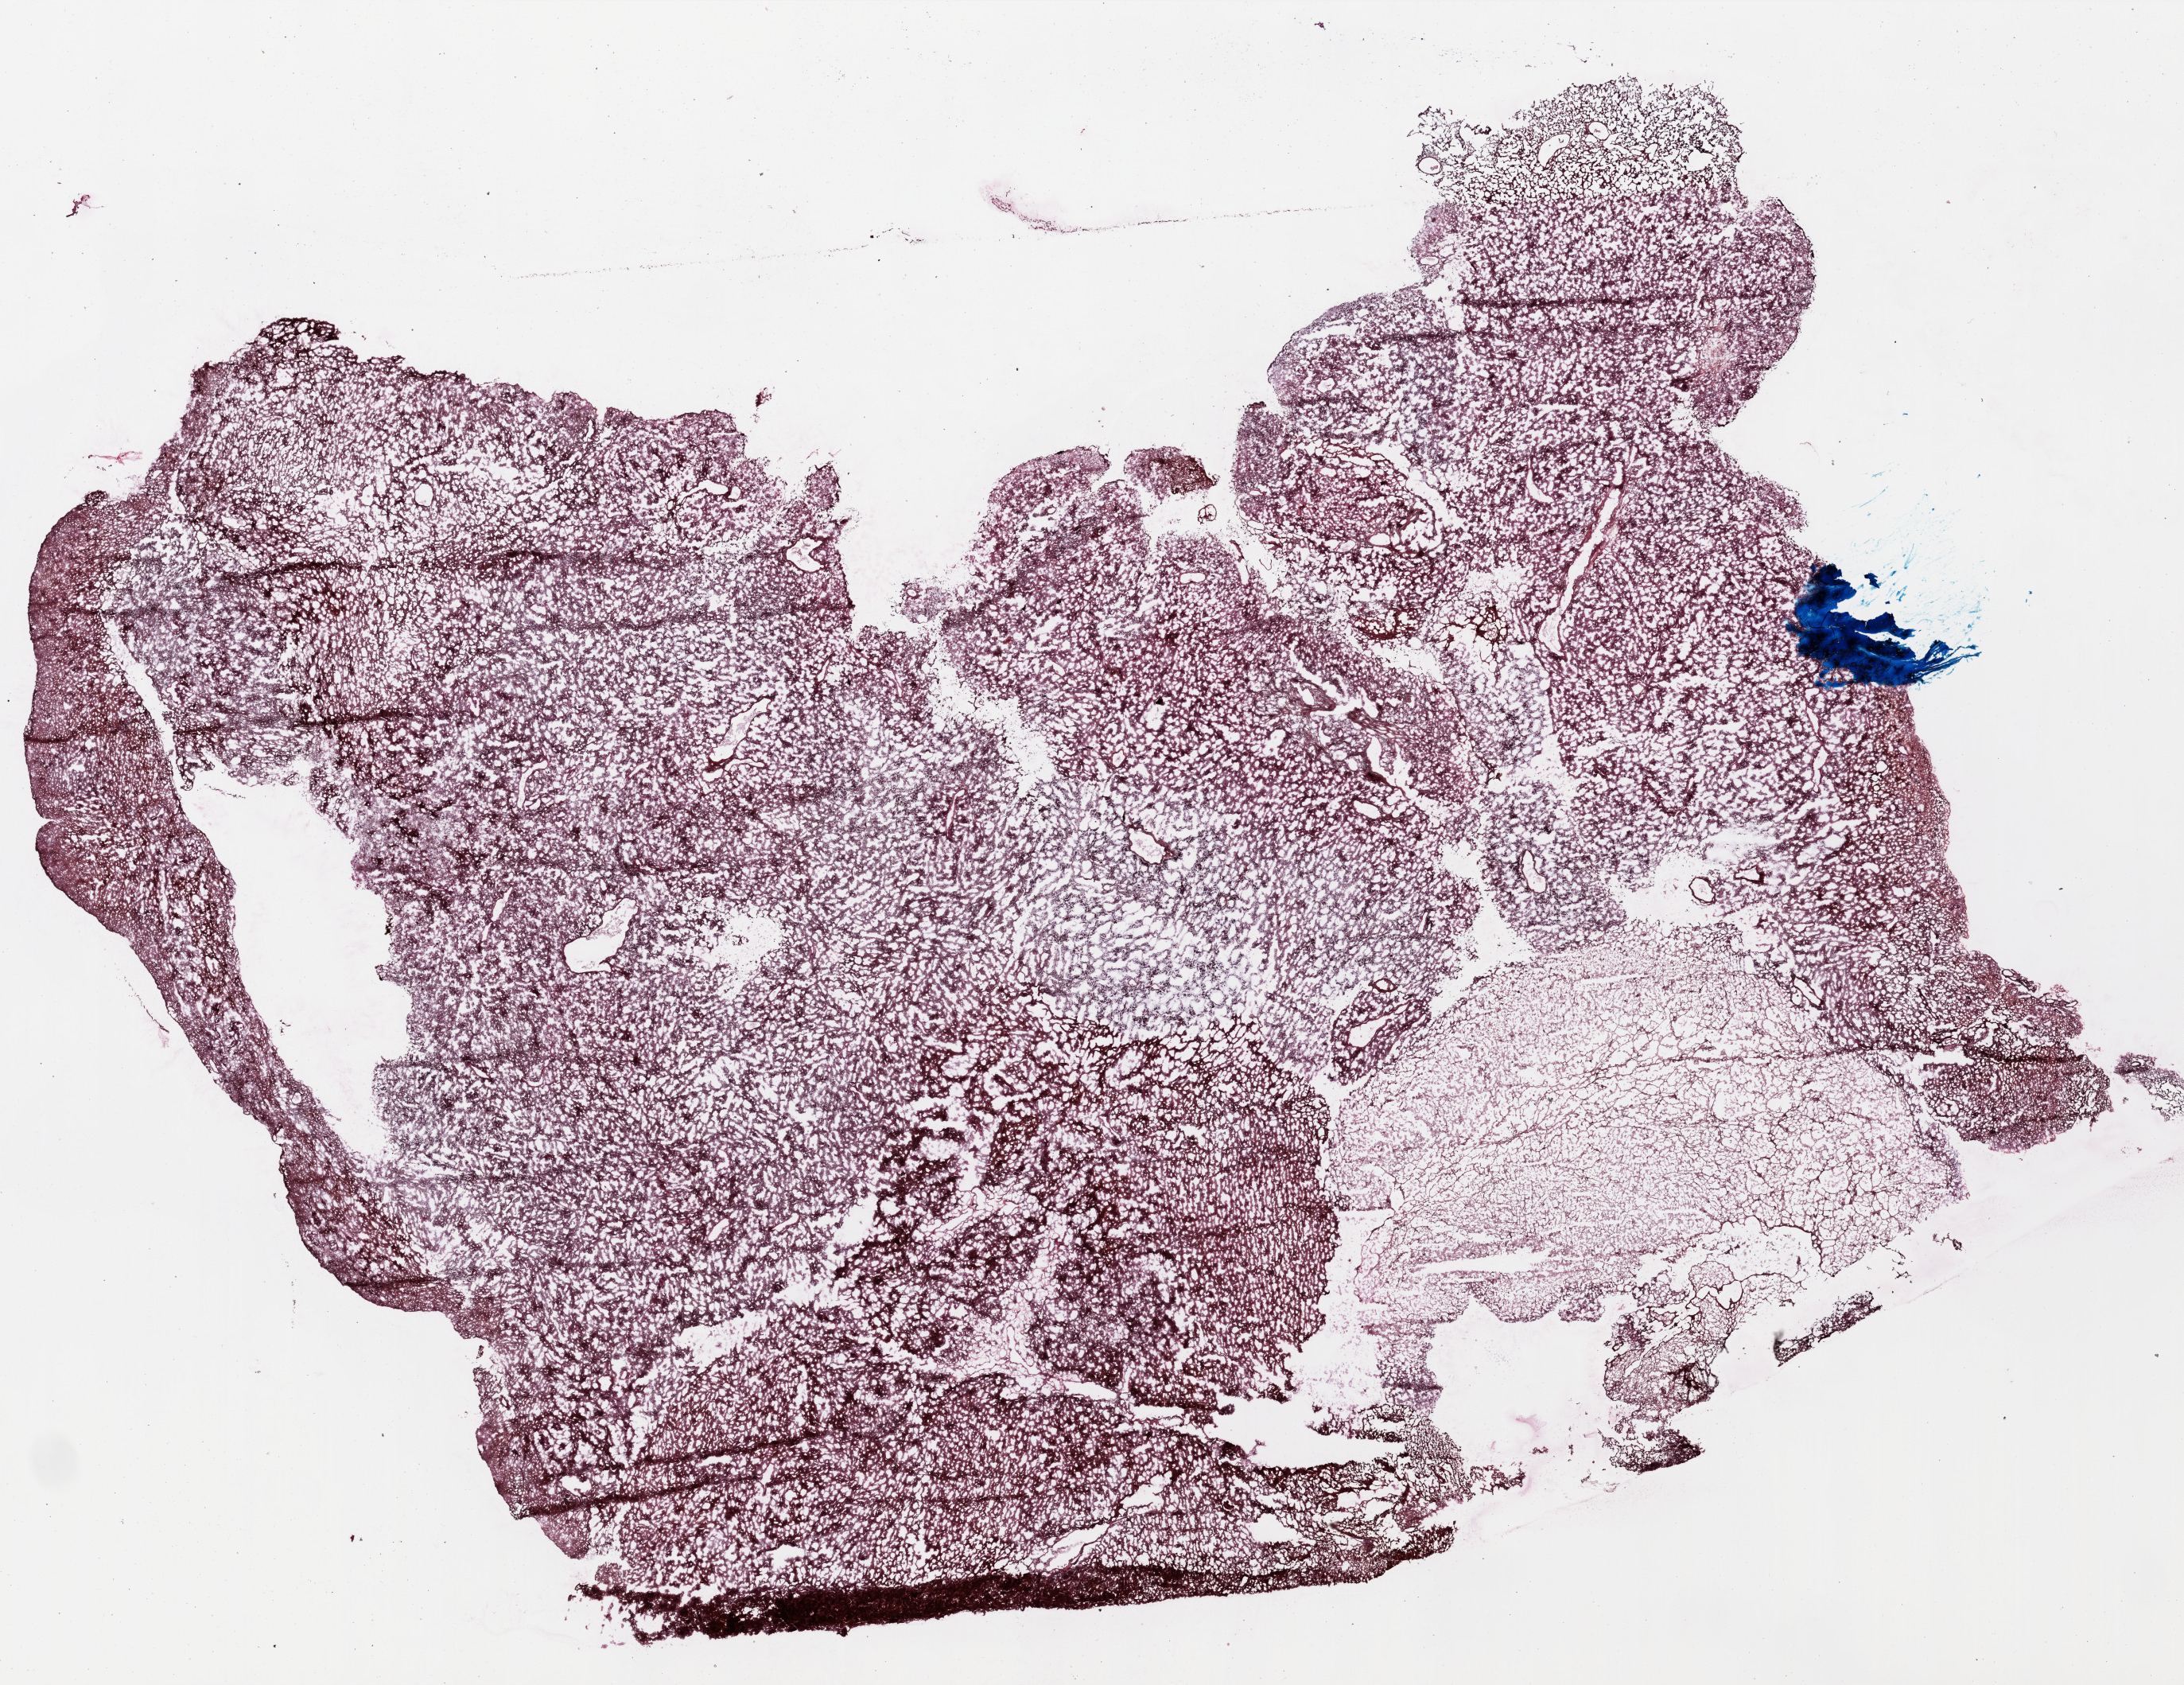
H&E-stained whole-slide image, a low-resolution overview of the entire scanned area, about 22.0 x 17.0 mm. Frozen section. Primary tumour sample from the brain. Male, age 48 years at initial diagnosis. Slide review estimates, as recorded: tumour cells 75%, tumour nuclei 95%, normal cells 0%, stromal cells 10%, necrosis 15%. Infiltration values recorded for this section: lymphocyte infiltration 0%.
Pathologic diagnosis: Glioblastoma.